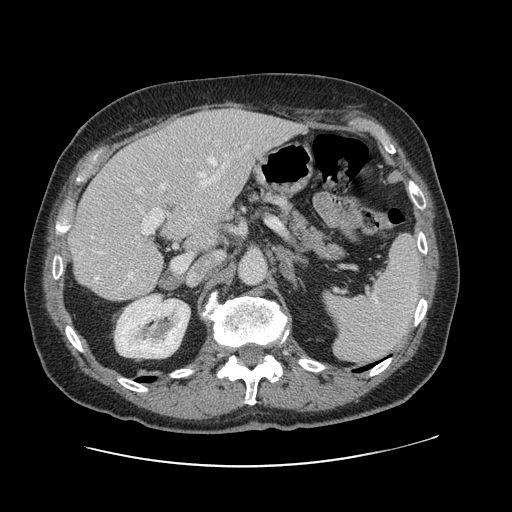
Contrast-enhanced abdominal CT, one axial slice. Slice 65 of 138 in the series (ordered by position). Intravenous contrast given. Soft-tissue window (W 400 / L 40 HU). 2.5 mm slice thickness. 512 × 512 image matrix. Male patient, age 71 years. From the clinical record (not read from this slice): diagnosis: colorectal cancer liver metastases, imaged before liver resection; multiple liver metastases: no; largest metastasis: 3.3 cm; chemotherapy before resection: no.
Structures marked on this image (outlined manually by an expert reader):
- hepatic veins: bounding box (x1, y1, x2, y2) in pixels: (91, 158, 226, 281)
- liver: (71, 108, 298, 300)
- planned liver remnant (the part of the liver to remain after resection): (71, 144, 216, 300)
- portal vein (with intrahepatic branches): (93, 145, 249, 255)